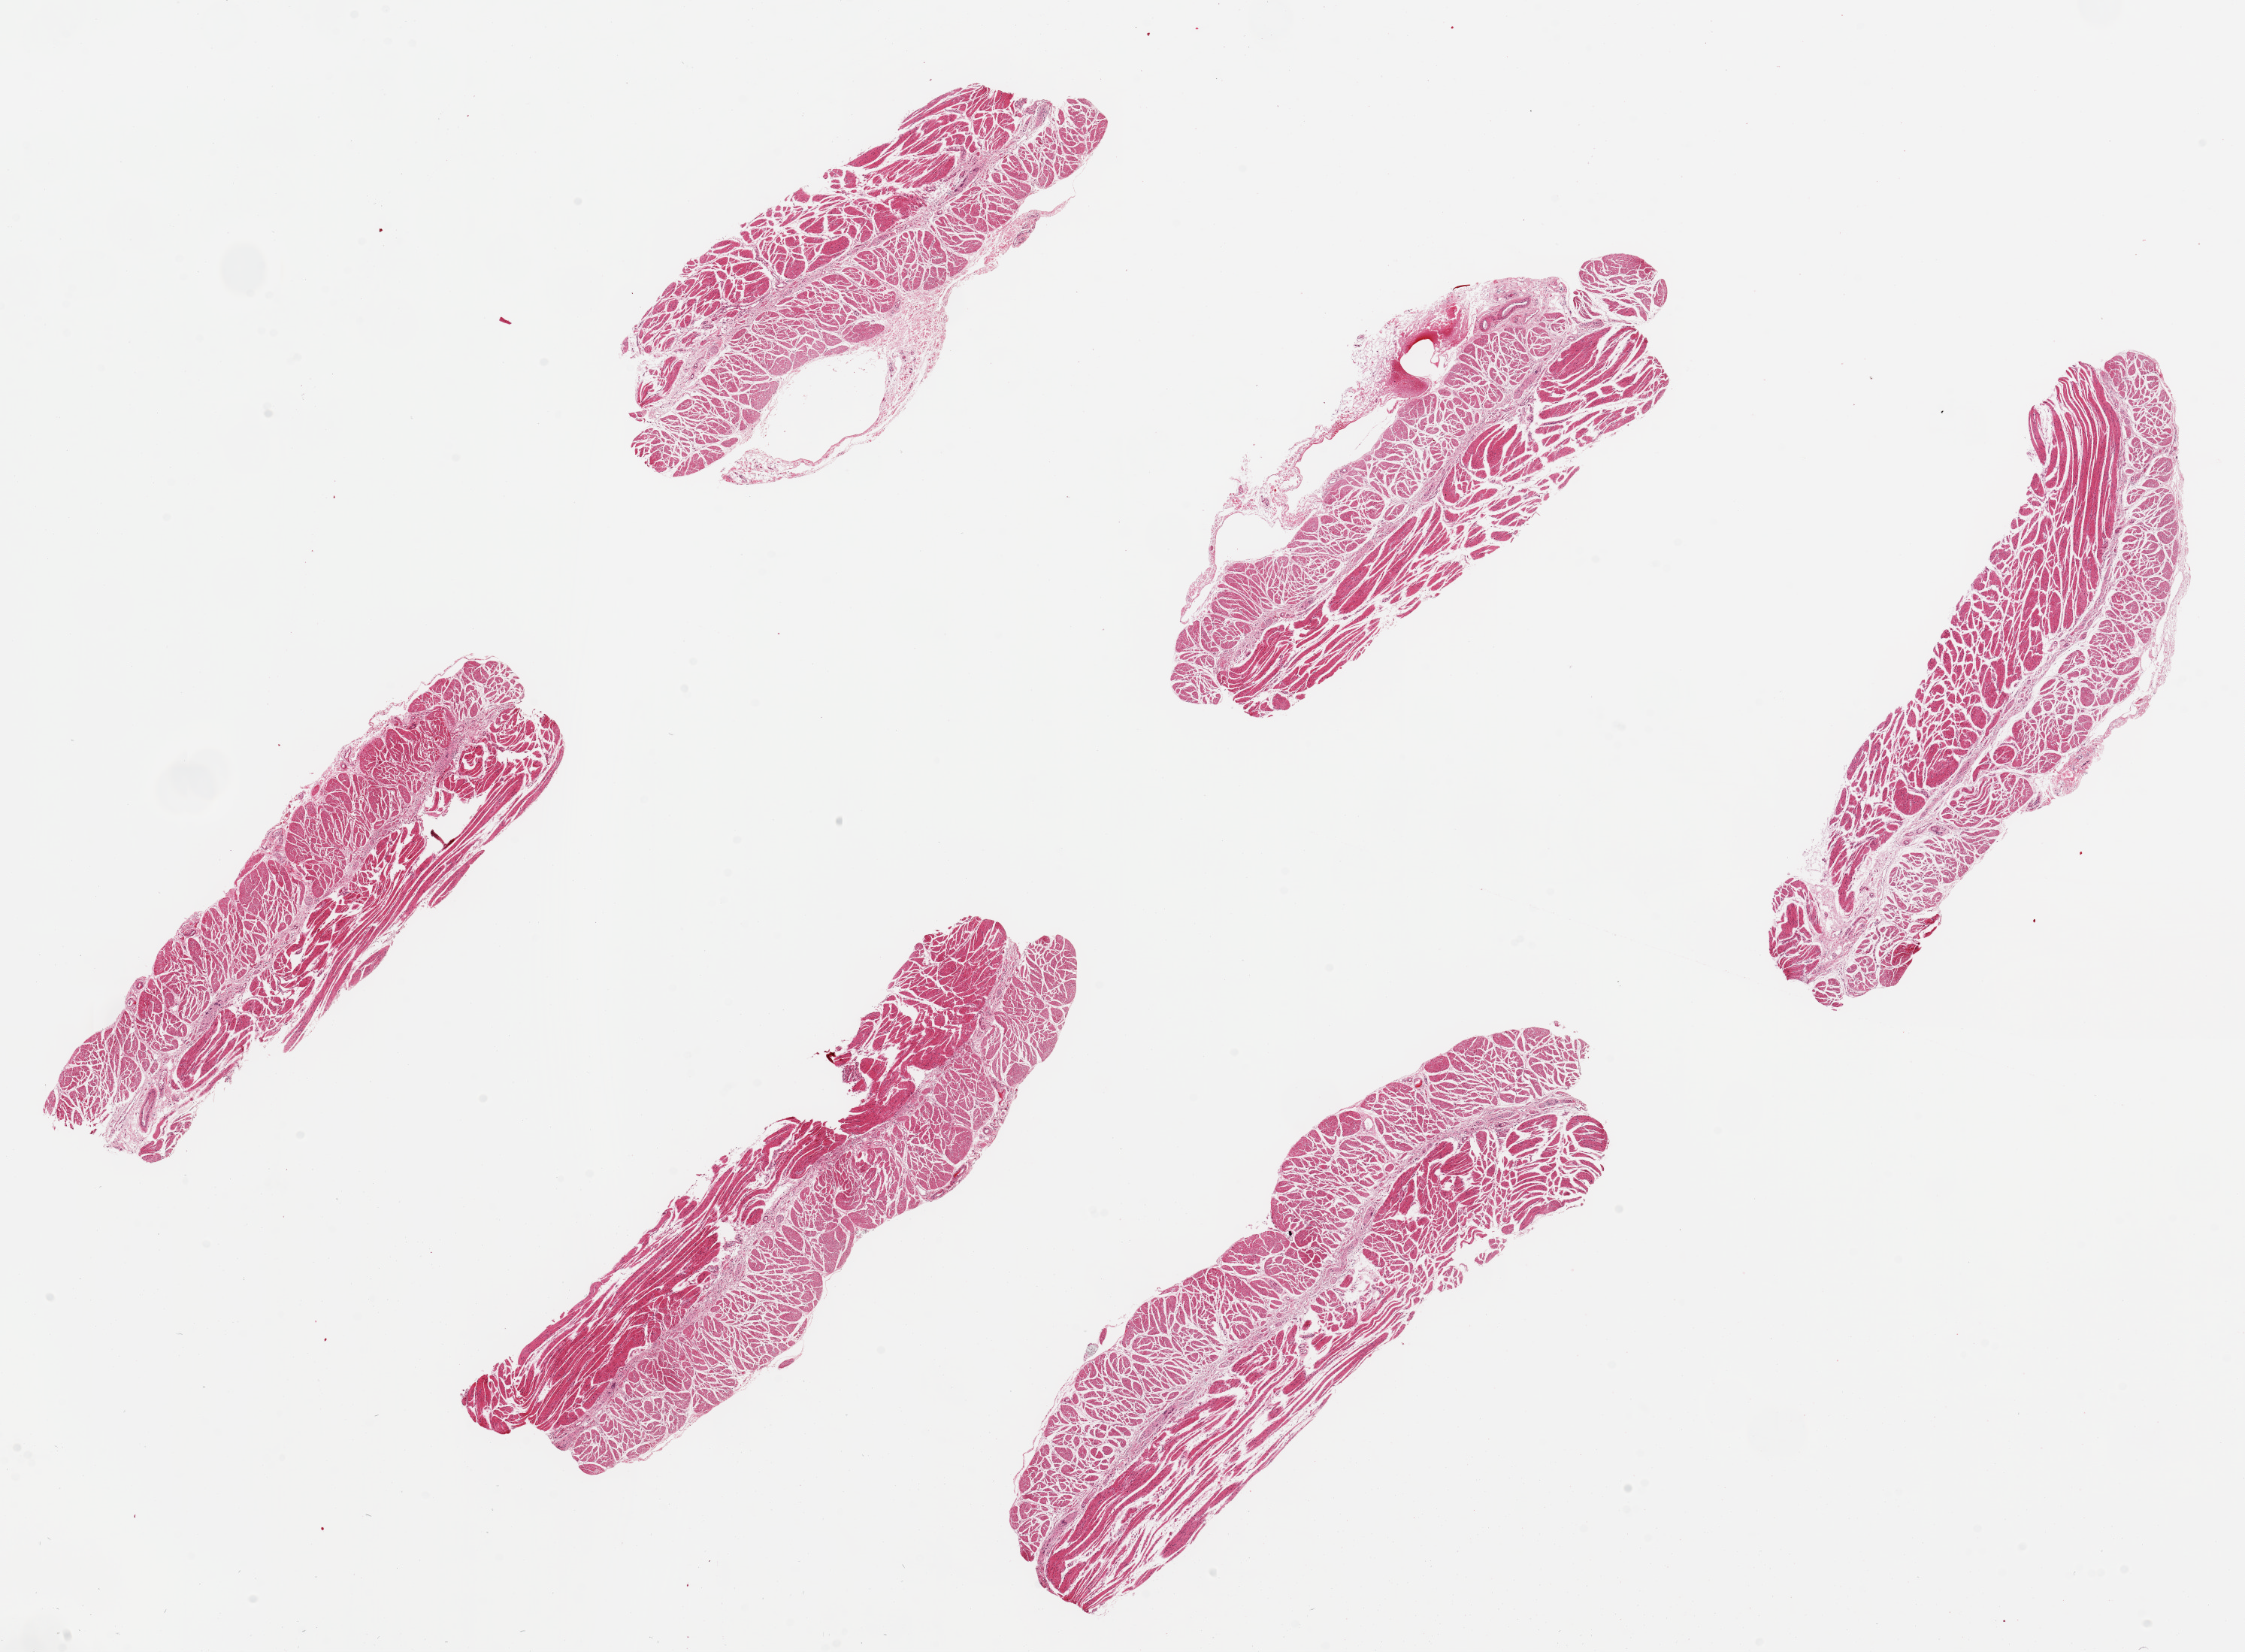
Digitized hematoxylin and eosin (H&E)-stained section, brightfield, low-resolution overview of the scanned area, about 23.6 x 17.4 mm (from a 20x scan), PAXgene-fixed, paraffin-embedded tissue, section of esophageal muscle (target tissue), donor tissue sample. Donor sex: male.
Review note (as recorded): 6 pieces, up to 7.5x2 mm.